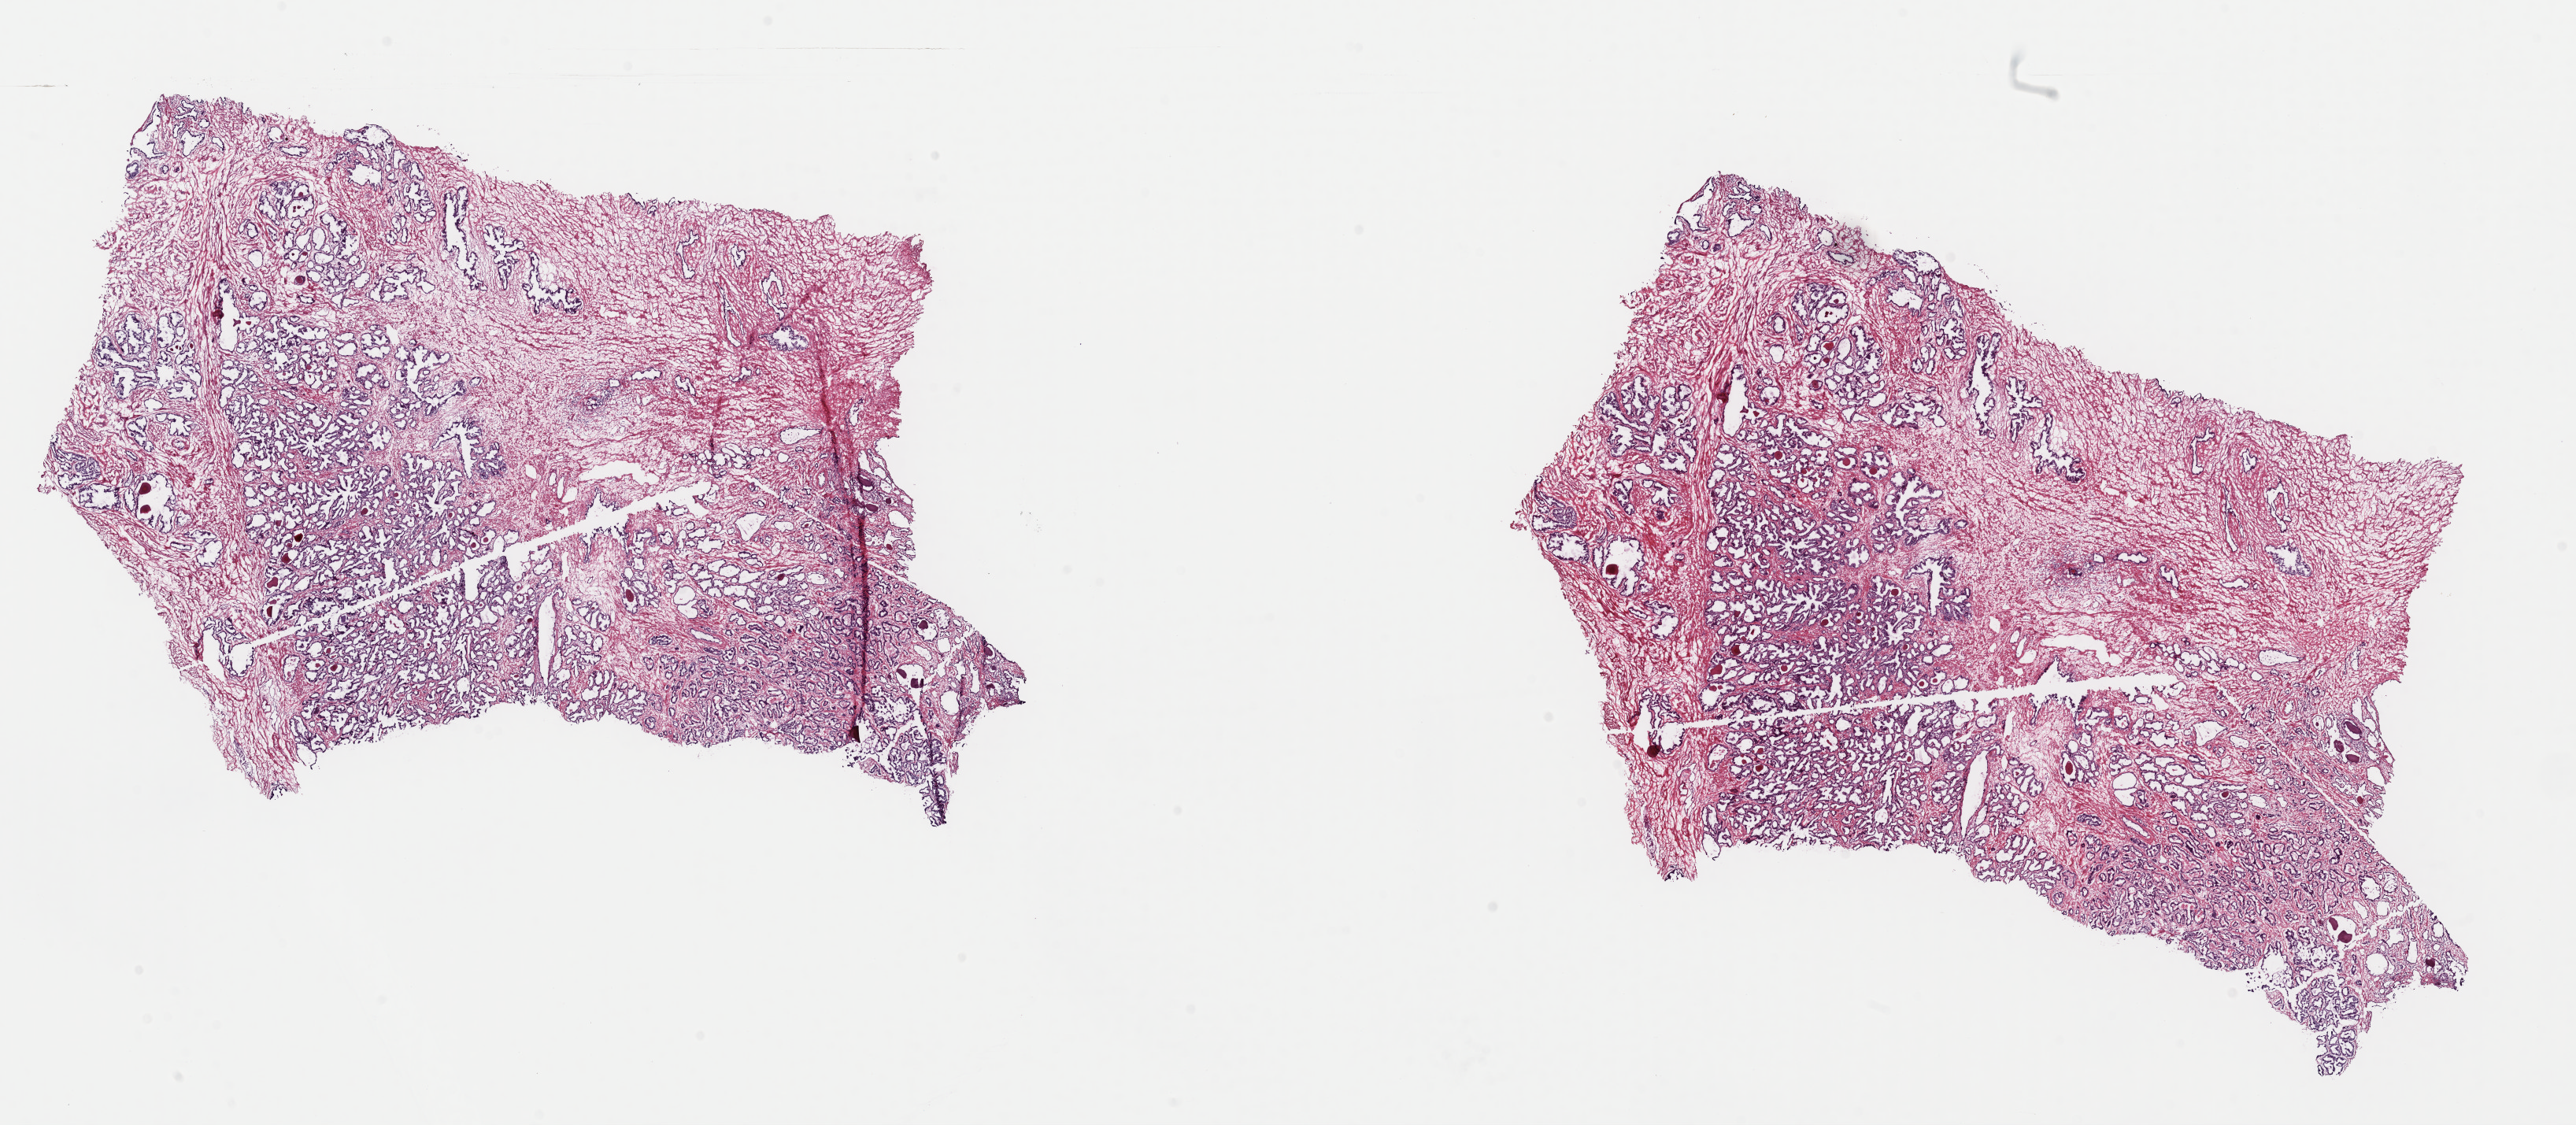
Hematoxylin and eosin (H&E) stained whole-slide image — shown as a low-resolution overview of the whole scanned area (about 25.8 x 11.3 mm, slide scanned at 40x), frozen section from the top of the tissue portion, prostate, primary tumour sample. Male patient; age at initial diagnosis 74 years. Gleason score: 7 (4+3). Pathologist review of this section (percent, as recorded): tumour cells 70%, tumour nuclei 70%, normal cells 30%, stromal cells 0%, necrosis 0%. Infiltration values recorded for this section: lymphocyte infiltration 1%, monocyte infiltration 0%, neutrophil infiltration 0%.
- lymph nodes positive (case pathology): 0 of 2 examined
- diagnosis: Adenocarcinoma, NOS (prostate gland)